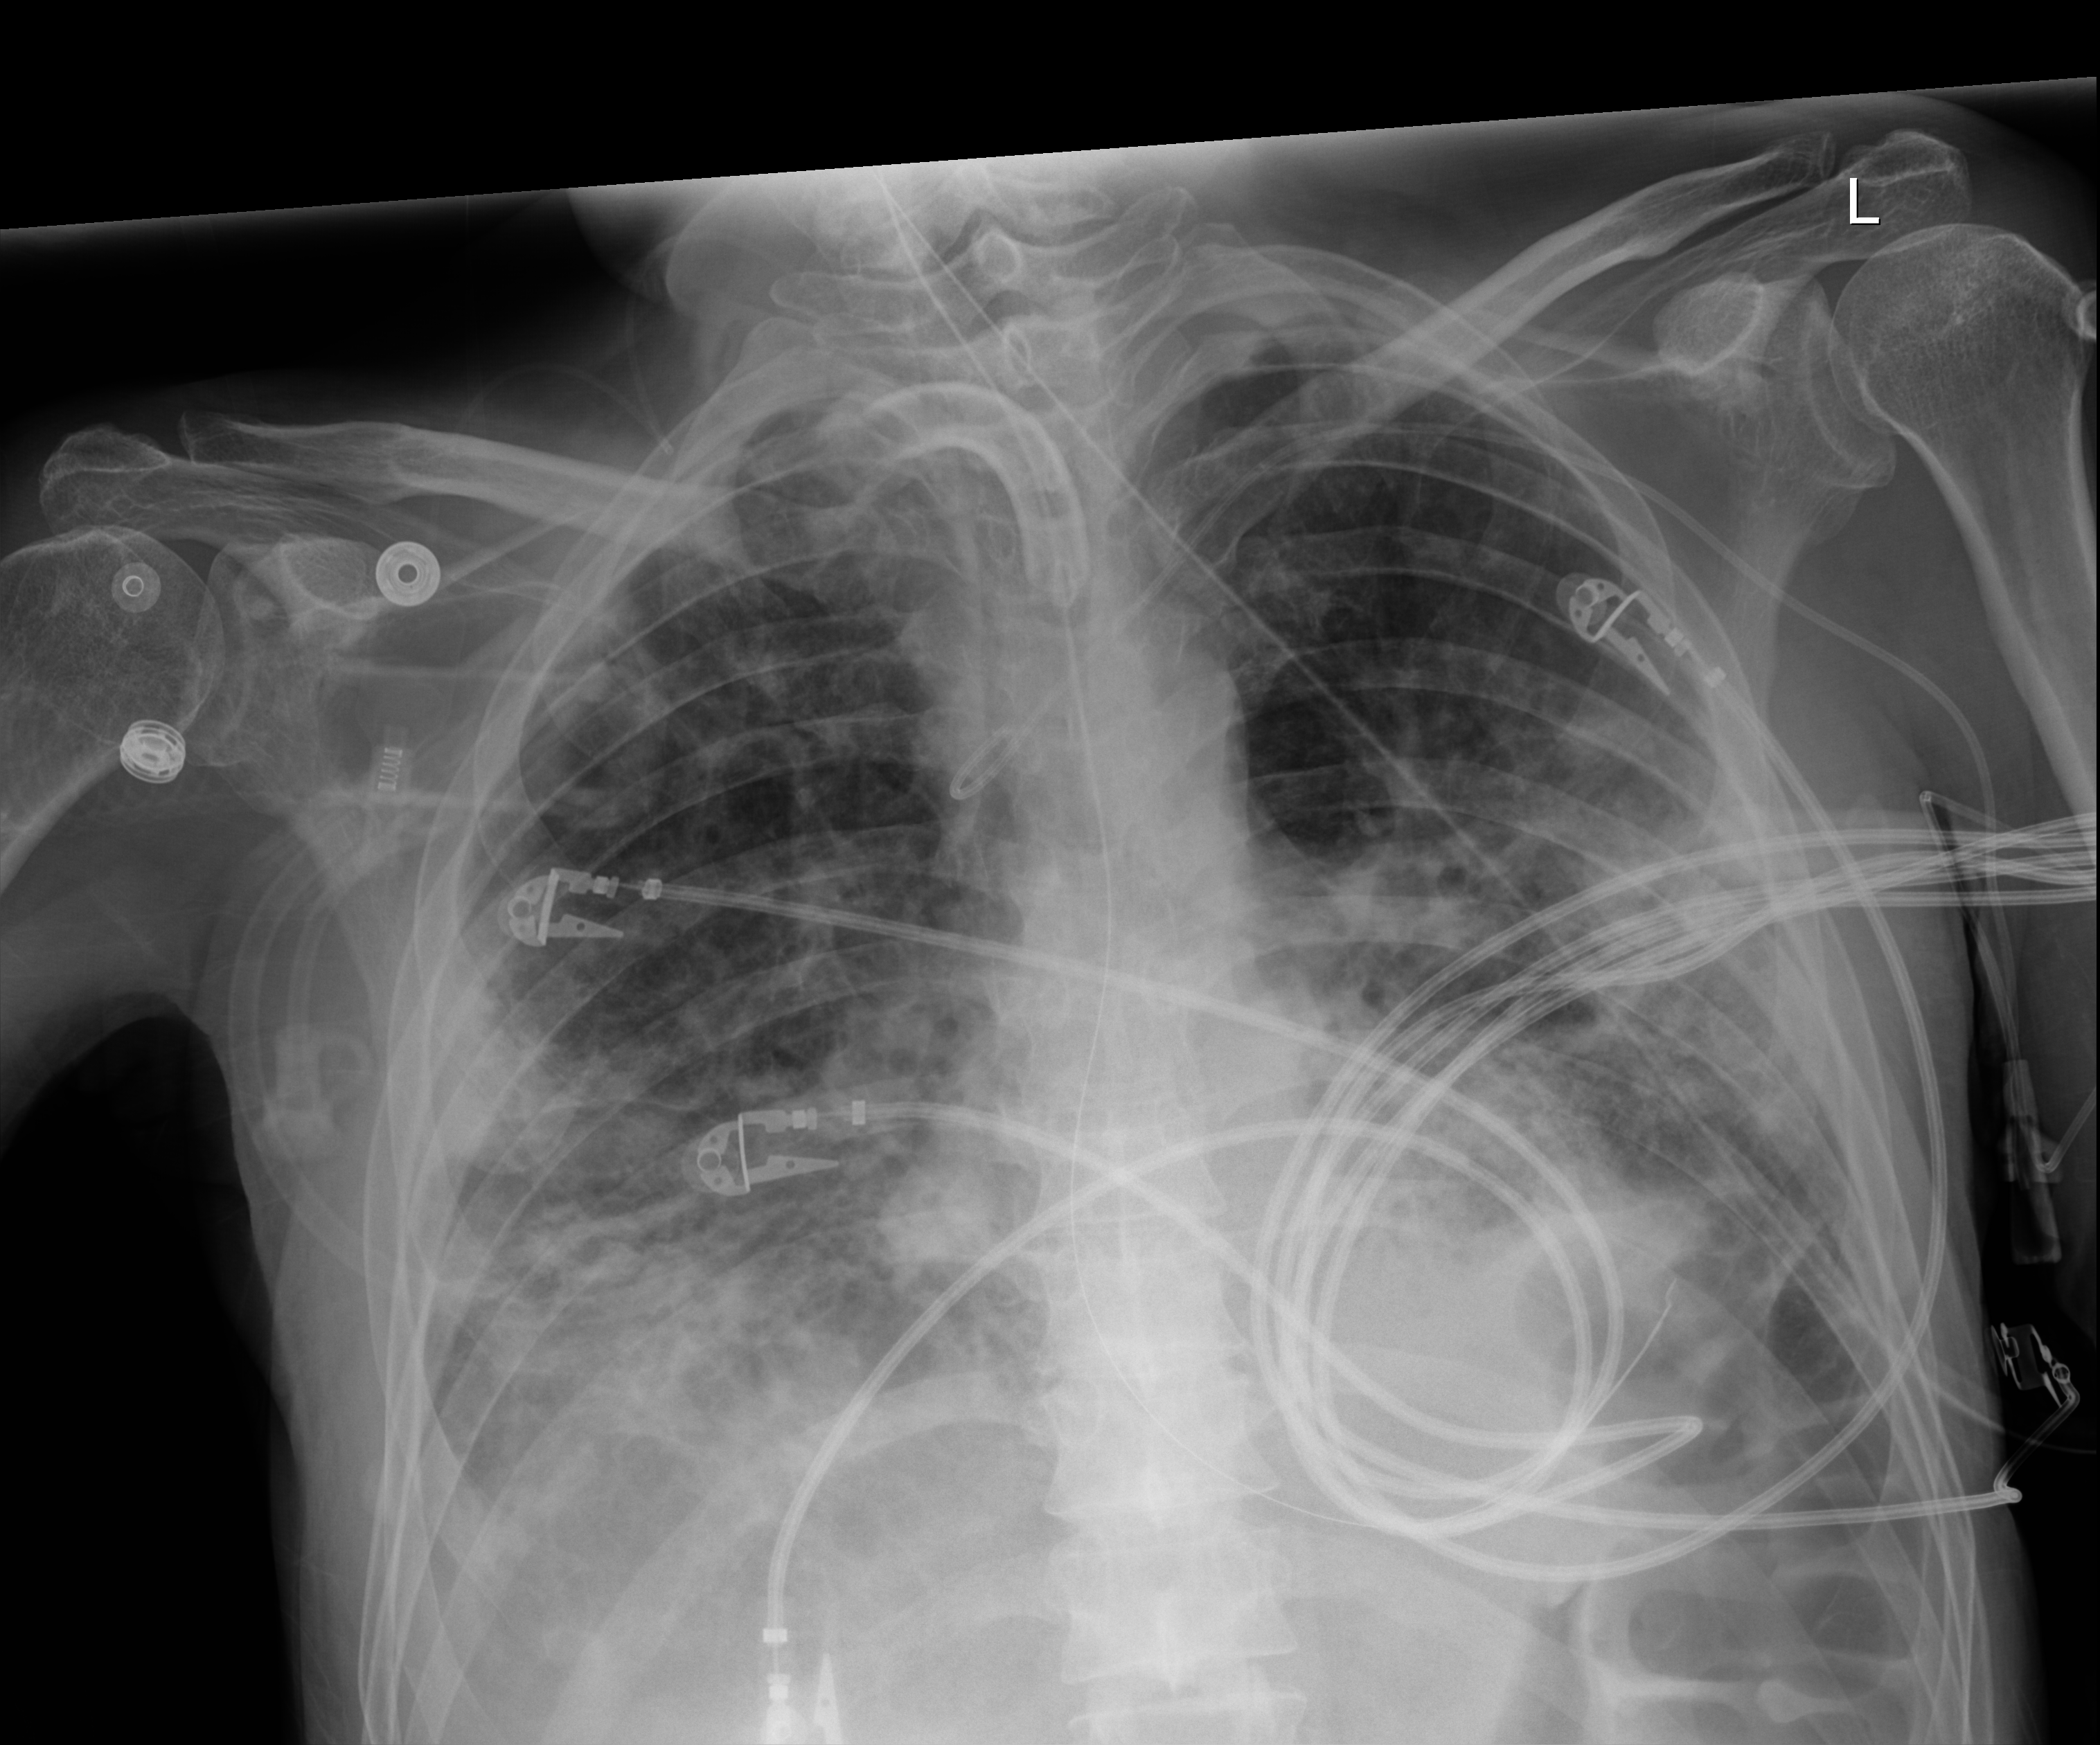
Chest X-ray; anteroposterior (AP) projection. Patient hospitalised with COVID-19; male, aged 18–59 years.
From the hospital-stay record, not from the radiograph (when in the stay this image was taken is not recorded): admitted to intensive care during this hospital stay: yes.